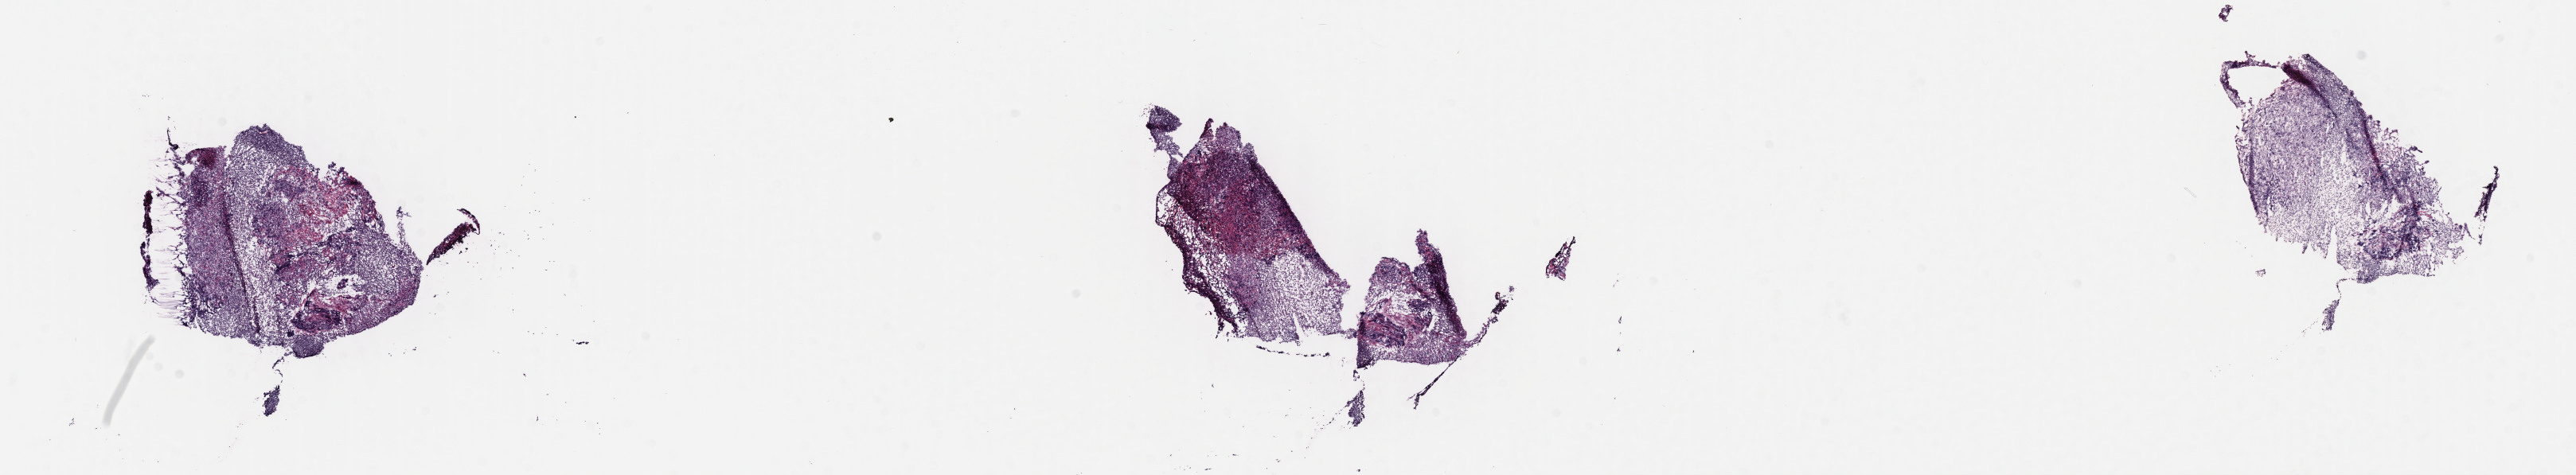
H&E whole-slide image — low-resolution overview of the scanned area, about 26.2 x 4.8 mm; cryosection; specimen: primary tumor; anatomic site: cranium. Male patient; age at initial diagnosis 6 years. Composition of this section per pathologist review: tumor cells 75%, tumor nuclei 90%, stromal cells 20%, necrosis 5%, normal cells 0%. Infiltration values recorded for this section: lymphocyte infiltration 3%, monocyte infiltration 5%, neutrophil infiltration 0%.
• diagnosis: Burkitt lymphoma, NOS
• section: top of the tissue portion
• Ann Arbor stage (patient): Stage IV